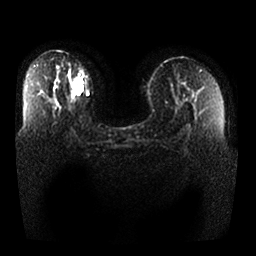
Breast MRI, one axial slice; slice 16 of 25 in the series (ordered by position); diffusion-weighted series; image 2 of 4 stored at this slice position (different b-values; order by instance number); 1.5 T; 256 × 256 image matrix. Female patient.
Annotated regions visible in this slice (outlined manually by an expert reader):
- tumour on diffusion-weighted imaging: bounding box (x1, y1, x2, y2) in pixels: (71, 77, 83, 92)